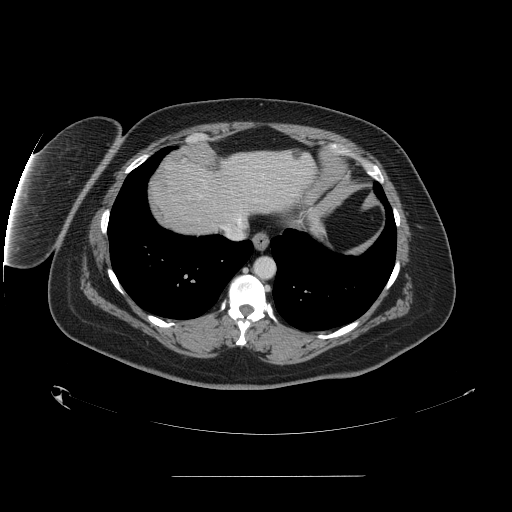
Contrast-enhanced abdominal CT, one axial slice; position 138 of 164 along the scan axis; 120 kVp; intravenous contrast given; soft-tissue window (W 400 / L 40 HU); 512 × 512 image matrix, field of view 495 × 495 mm. Female patient, age 52 years. From the clinical record (not read from this slice): diagnosis: colorectal cancer liver metastases, imaged before liver resection; multiple liver metastases: yes; largest metastasis: 3.5 cm; disease in both lobes: no.
Outlined on this slice (manually delineated by an expert):
- hepatic veins: bounding box [x1, y1, x2, y2] px = [221, 206, 245, 240]
- liver: [151, 149, 315, 235]
- planned liver remnant (the part of the liver to remain after resection): [179, 149, 315, 225]
- liver metastasis: [294, 155, 302, 160]